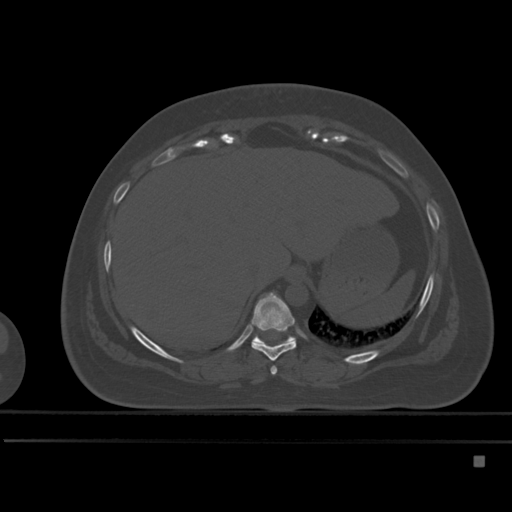
CT including the spine, one axial slice; position 259 of 495 along the scan axis; bone window (W 1800 / L 400 HU); 1.5 mm slice thickness; 512 × 512 image matrix, field of view 404 × 404 mm. Female patient, age 33 years. Case-level facts recorded for this patient, not image findings: primary cancer: breast; vertebrae with lytic lesions (as recorded): T1.
Annotated regions visible in this slice (semi-automatically segmented with operator editing):
- T10 vertebra: box from (x=252, y=336) to (x=295, y=344) px
- T8 vertebra: (x=271, y=366)–(x=277, y=375)
- T9 vertebra: (x=250, y=292)–(x=297, y=361)